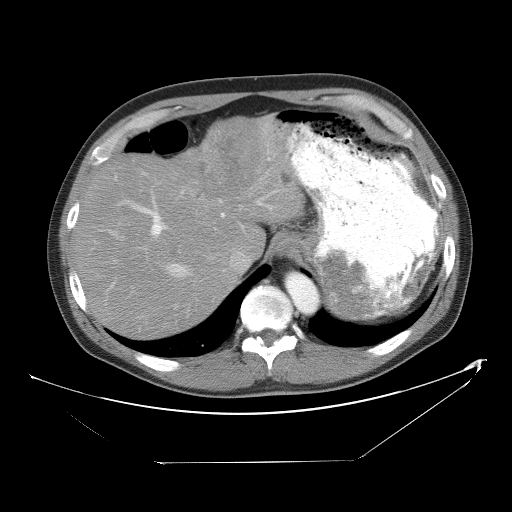
Contrast-enhanced abdominal CT, one axial slice. Slice 40 of 53 in the series (ordered by position). Reconstruction kernel STANDARD. 120 kVp. Soft-tissue window (W 400 / L 40 HU). 5 mm slice thickness. 512 × 512 image matrix. Male patient, age 59 years. Case-level facts recorded for this patient, not image findings: diagnosis: colorectal cancer liver metastases, imaged before liver resection; multiple liver metastases: yes; largest metastasis: 8.5 cm; disease in both lobes: no.
Outlined on this slice (manually delineated by an expert):
- hepatic veins: bounding box (x1, y1, x2, y2) in pixels: (166, 190, 250, 278)
- liver: (76, 120, 301, 337)
- planned liver remnant (the part of the liver to remain after resection): (76, 159, 233, 337)
- portal vein (with intrahepatic branches): (119, 190, 279, 239)
- liver metastasis: (282, 174, 290, 187)
- liver metastasis: (167, 250, 180, 258)
- liver metastasis: (219, 137, 241, 170)